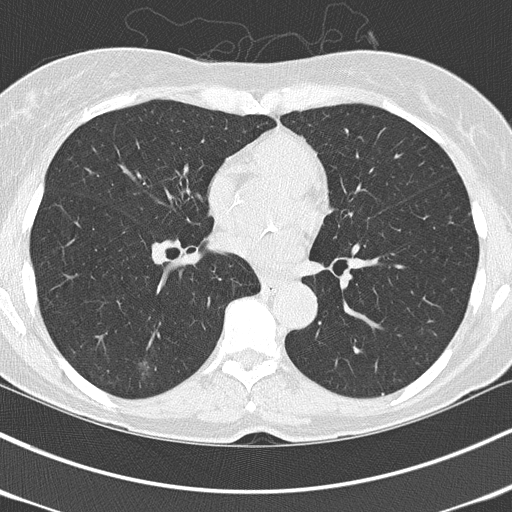
Chest CT (low-dose screening protocol), one axial image; third screening round (two years after baseline); lung window (W 1500 / L -600 HU); 2 mm slice thickness; slice 84 of 150 in the series; 512 × 512 image matrix, field of view 318 × 318 mm. Female participant, aged 67 years at enrolment. Current smoker at enrolment.
- Expert reader's lesion annotation, box from (x=126, y=347) to (x=167, y=387) px.
- The screening reader recorded 3 non-calcified nodules or masses ≥4 mm on this exam (right lower lobe, right lower lobe, left lower lobe); which of them this box marks is not recorded.
- Official screen result: positive, other.
- Later outcome: lung cancer diagnosed 64 days after this screen — adenocarcinoma, NOS, left lower lobe, poorly differentiated (G3), stage IA (AJCC 6th edition), 25 mm at pathology.